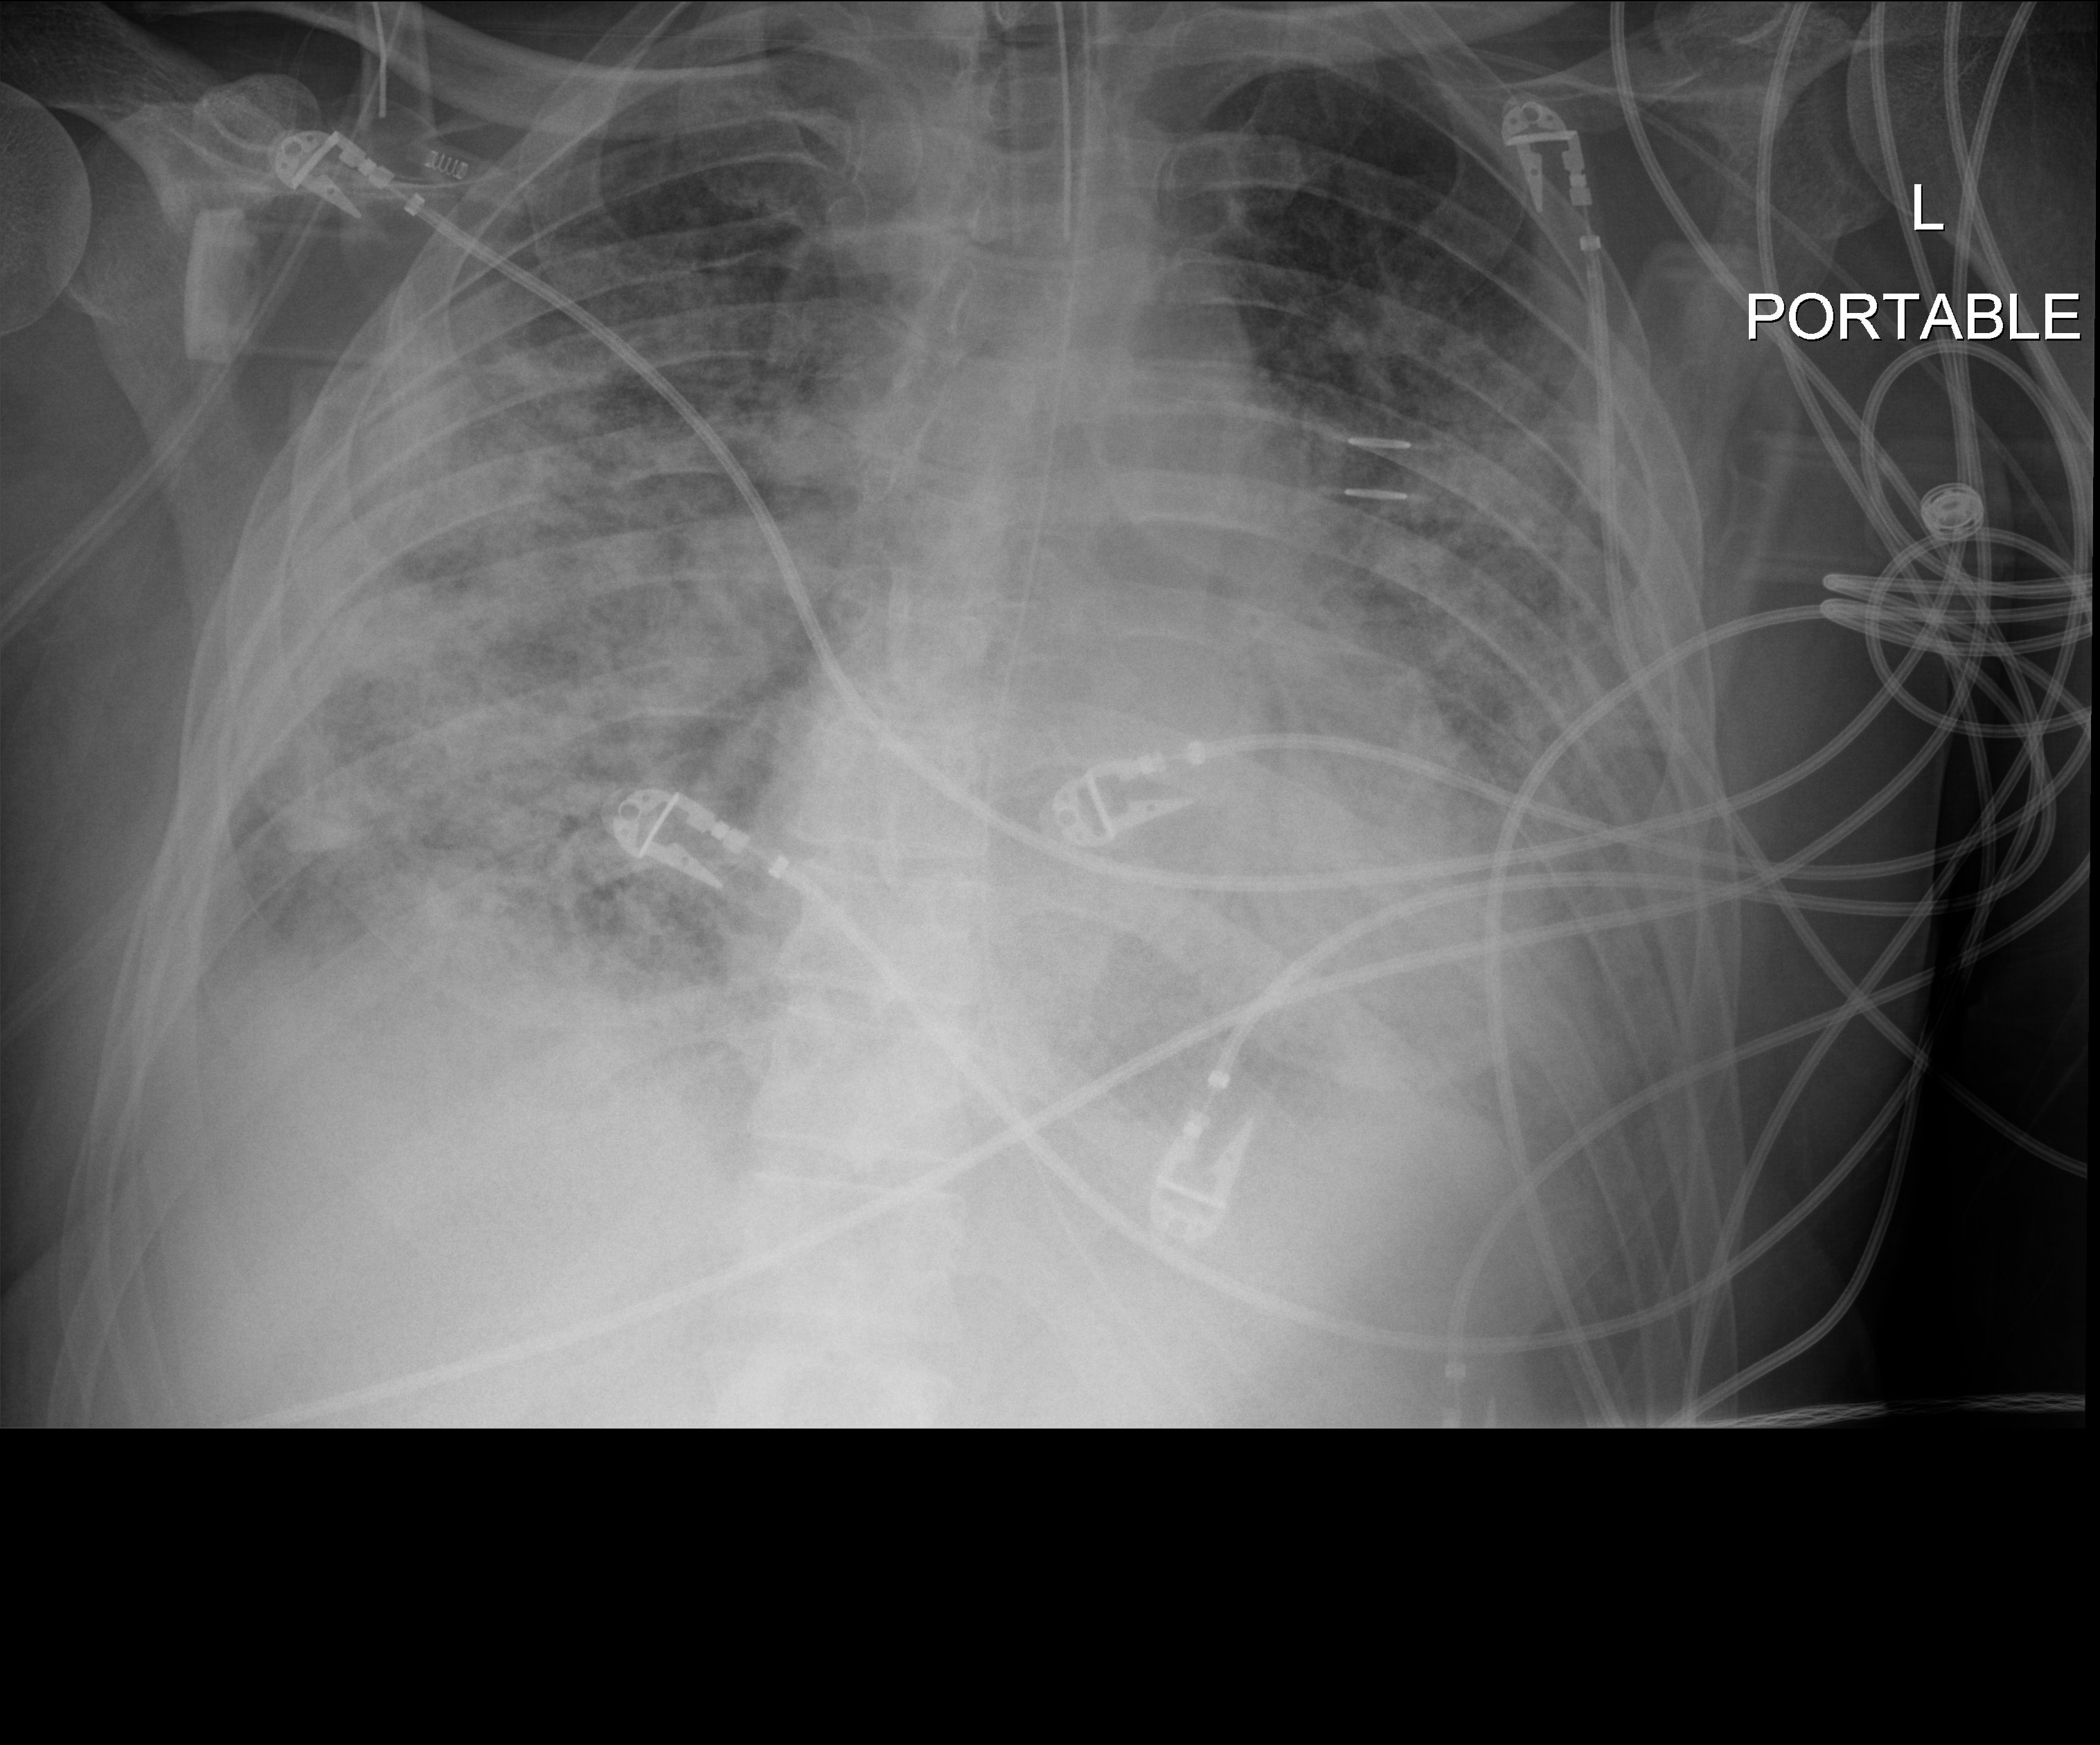
Bedside chest radiograph (digital radiography), anteroposterior (AP) projection. Male patient hospitalised with COVID-19, age 18–59 years.
Hospital-stay facts (about this admission, not read from this image; timing relative to this image not recorded): admitted to intensive care during this hospital stay: yes.